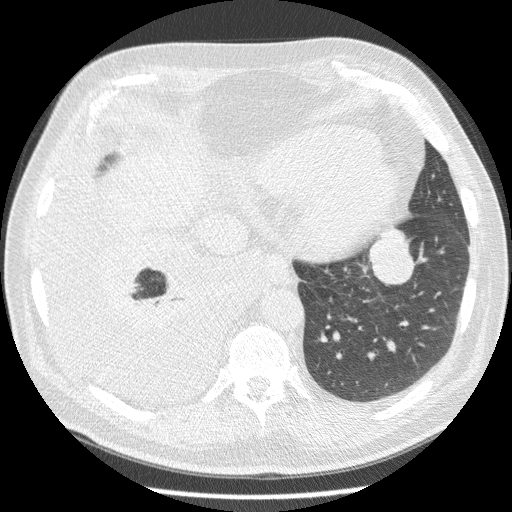
Low-dose screening chest CT, one axial slice; position 56 of 180 along the scan axis; reconstruction kernel STANDARD; 120 kVp; lung window (W 1500 / L -600 HU); 2.5 mm slice thickness; 512 × 512 image matrix, field of view 355 × 355 mm.
Annotated regions visible in this slice (outlined manually by an expert reader):
- lesion 1 (tumor, lower lobe of left lung): bounding box (x1, y1, x2, y2) in pixels: (366, 226, 421, 285)